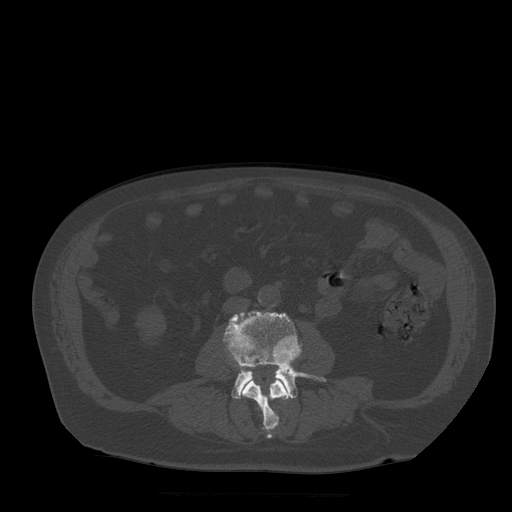
CT including the spine, one axial slice. Position 127 of 522 along the scan axis. Bone window (W 1800 / L 400 HU). 512 × 512 image matrix. Patient age 72 years. Case-level facts recorded for this patient, not image findings: primary cancer: prostate.
Outlined on this slice (semi-automatic segmentation, software-assisted and operator-edited):
- L3 vertebra: bounding box [x1, y1, x2, y2] px = [240, 377, 291, 439]
- L4 vertebra: [225, 312, 326, 399]